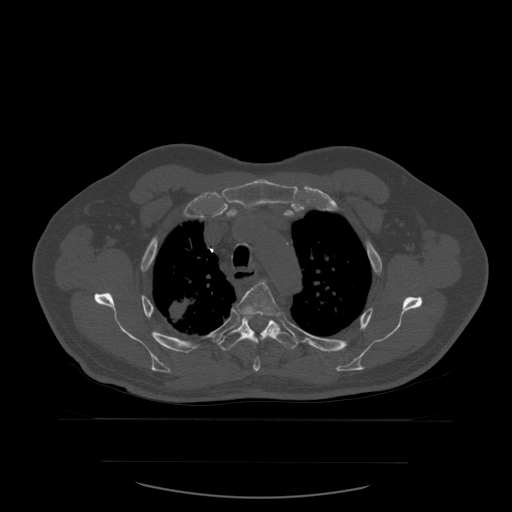
CT including the spine, one axial slice; slice 434 of 590 in the series (ordered by position); bone window (W 1800 / L 400 HU); 1.25 mm slice thickness; 512 × 512 image matrix, field of view 479 × 479 mm. Patient age 71 years. Case-level facts recorded for this patient, not image findings: primary cancer: lung.
Annotated regions visible in this slice (semi-automatically segmented with operator editing):
- T4 vertebra: bounding box (x1, y1, x2, y2) in pixels: (236, 281, 281, 372)
- T5 vertebra: (218, 314, 299, 351)